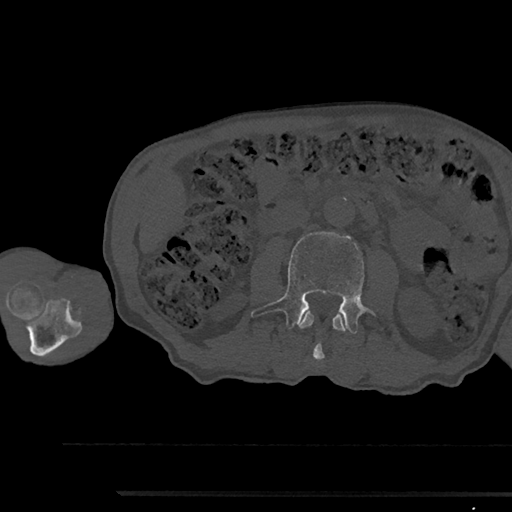
CT including the spine, one axial slice; slice 512 of 797 in the series (ordered by position); reconstruction kernel Br40s/3; 120 kVp; bone window (W 1800 / L 400 HU); 0.5 mm slice thickness; 512 × 512 image matrix, field of view 367 × 367 mm. Male patient, age 79 years. From the clinical record (not read from this slice): primary cancer: prostate.
Annotated regions visible in this slice (semi-automatic segmentation, software-assisted and operator-edited):
- L2 vertebra: bounding box <298,311,347,361> (left, top, right, bottom; pixels)
- L3 vertebra: <251,232,376,333>